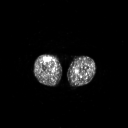
FDG PET of an extremity soft-tissue mass (from a PET/CT study), one axial slice. Position 245 of 311 along the scan axis. 128 × 128 image matrix, field of view 700 × 700 mm. Male patient, age 56 years. From the clinical record (not read from this slice): histological type: pleiomorphic leiomyosarcoma; grade: intermediate; site of the primary tumour: right thigh.
Structures marked on this image (expert contour drawn on MRI and transferred to this co-registered scan by the dataset authors):
- gross tumour volume including surrounding oedema: bounding box [x1, y1, x2, y2] px = [44, 57, 51, 62]